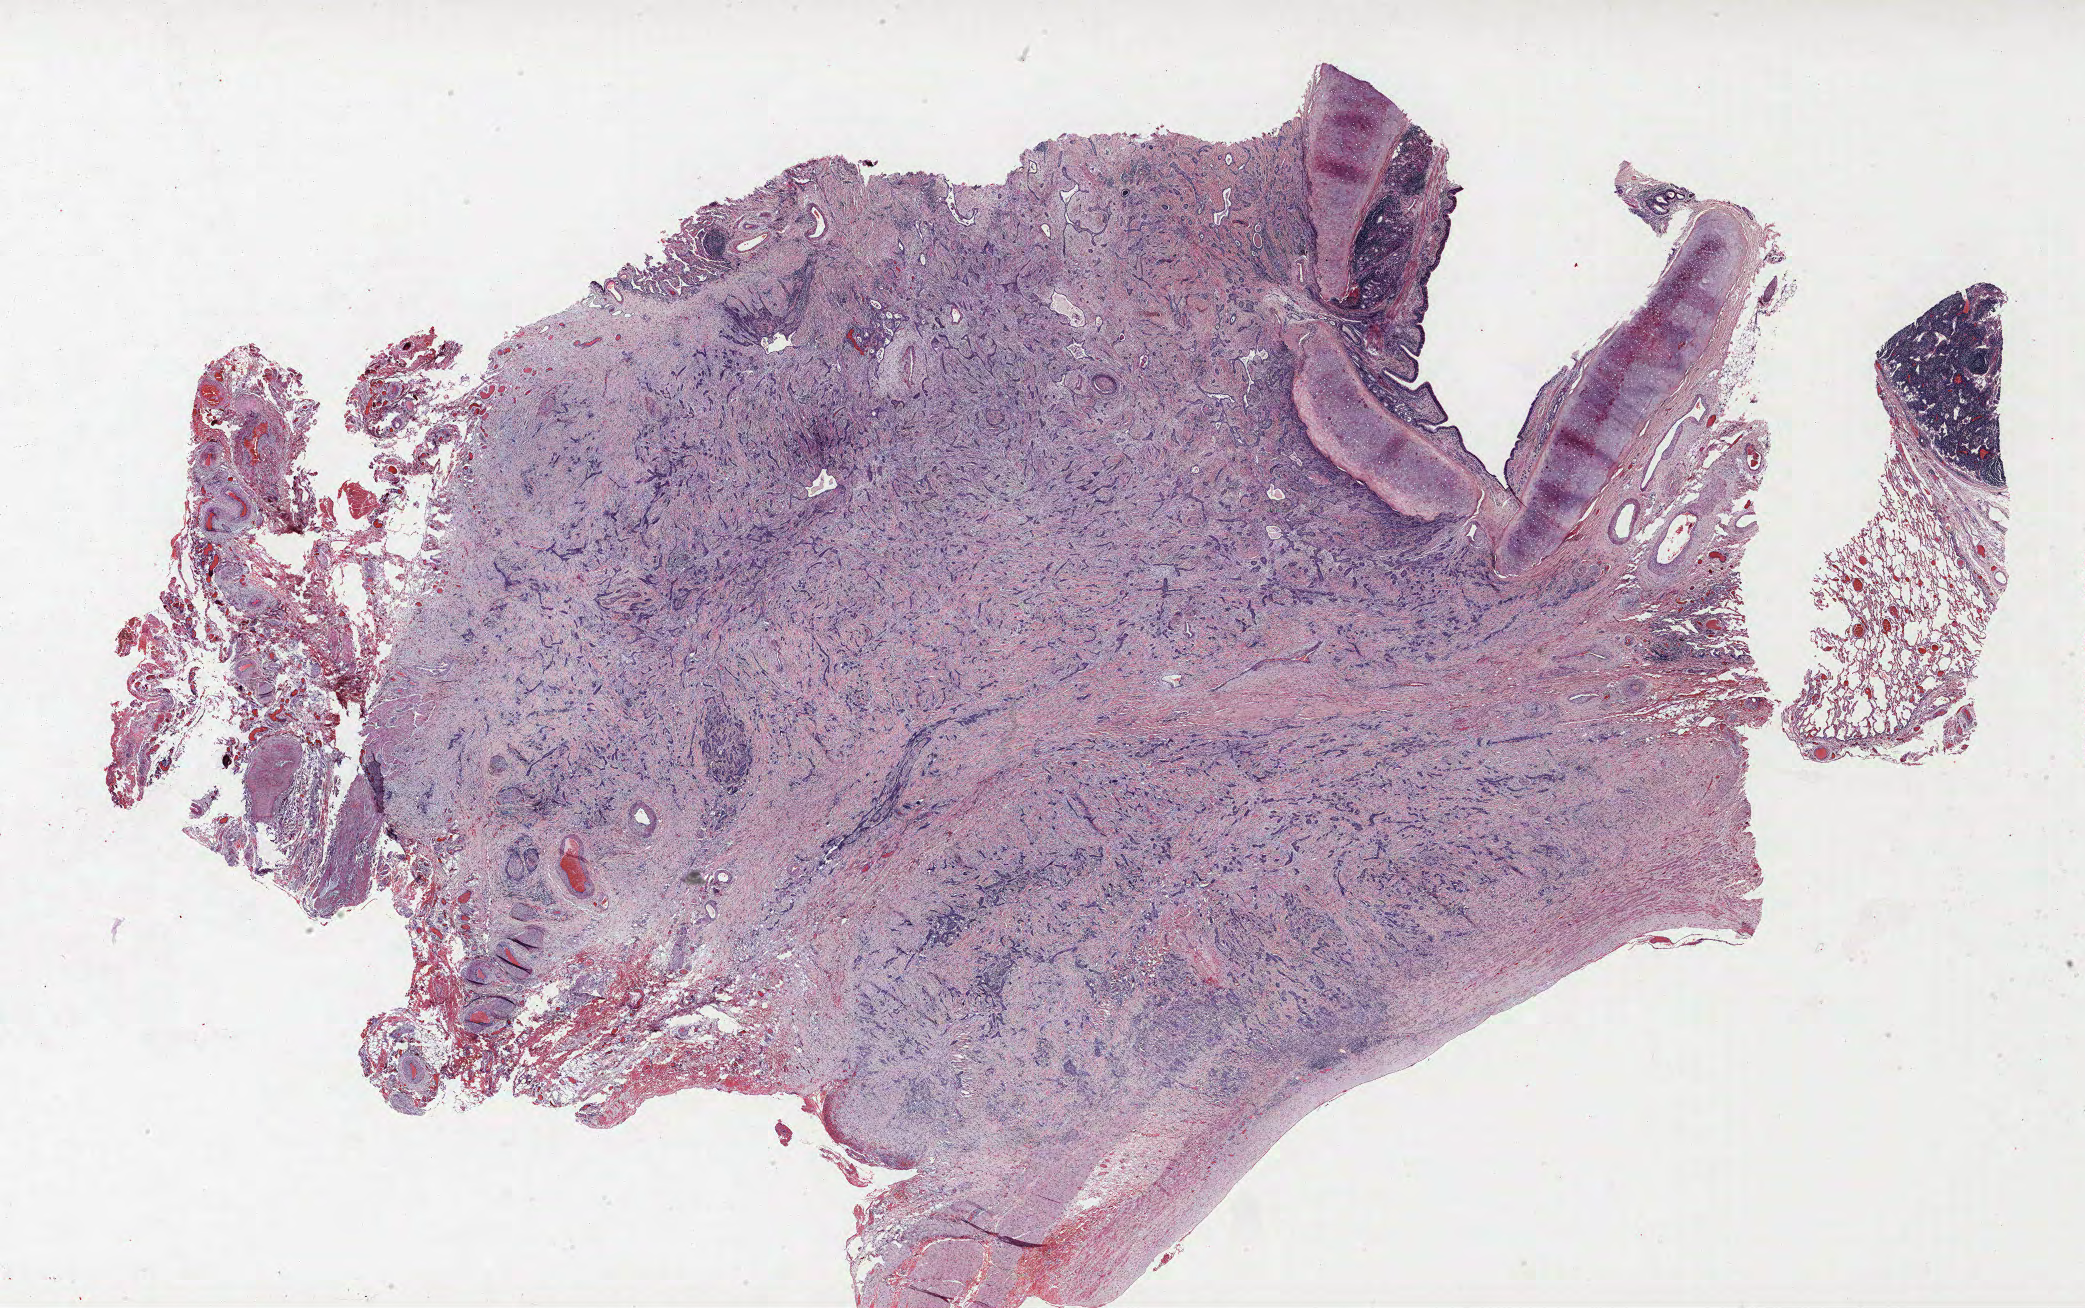
Whole-slide histology image, H&E, shown as a low-resolution overview of the whole scanned area (about 33.4 x 20.9 mm, from a 40x scan). FFPE section. Lung tissue. Female patient, aged 62 at enrolment. Former smoker at enrolment. Grade: poorly differentiated (G3).
Tumour size (pathology): 50 mm. Stage (AJCC 6th edition): IIIB. Primary tumour location (clinical record): left hilum. Participant's lung-cancer diagnosis: Squamous cell carcinoma, NOS.